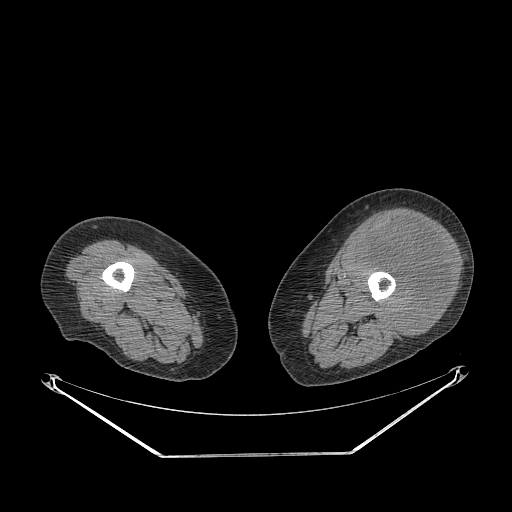
CT of an extremity soft-tissue mass (from a PET/CT study), one axial slice. Slice 219 of 267 in the series (ordered by position). 140 kVp. Soft-tissue window (W 400 / L 40 HU). 512 × 512 image matrix, field of view 500 × 500 mm. Female patient. Case-level facts recorded for this patient, not image findings: histological type: undifferentiated – high grade; grade: high; site of the primary tumour: left thigh.
Outlined on this slice (expert contour drawn on MRI and transferred to this co-registered scan by the dataset authors):
- gross tumour volume including surrounding oedema: bounding box <358,217,455,336> (left, top, right, bottom; pixels)
- gross tumour volume (mass): <358,217,453,336>